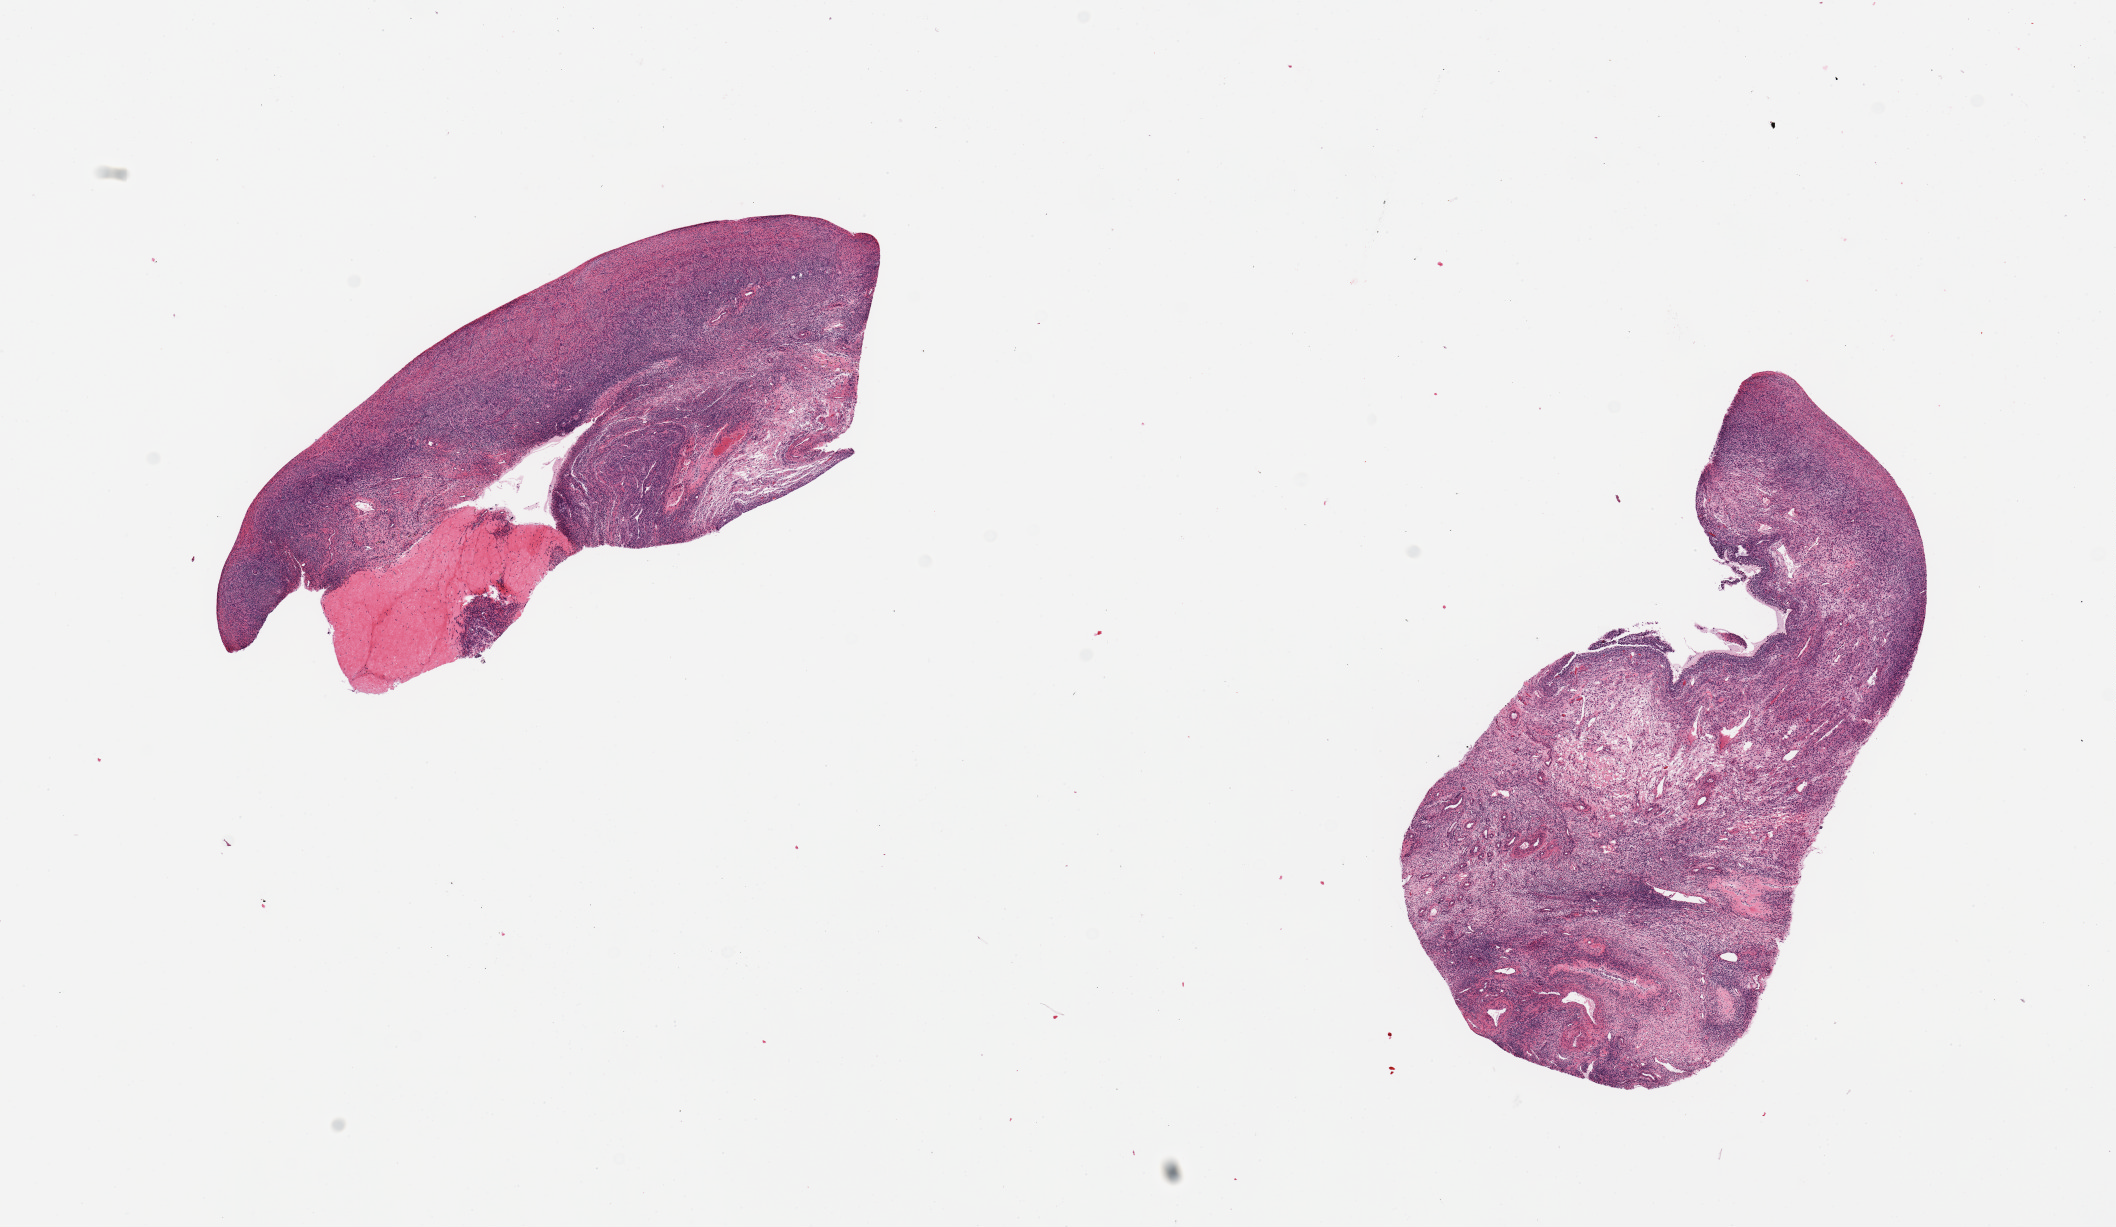
Whole-slide image, H&E stain, brightfield, shown as a low-resolution overview of the whole scanned area (about 16.7 x 9.7 mm, slide scanned at 20x), PAXgene-fixed, paraffin-embedded tissue, section of ovary (target tissue), tissue donor sample. Donor sex: female.
Pathologist's review note for this sample: 2 pieces.